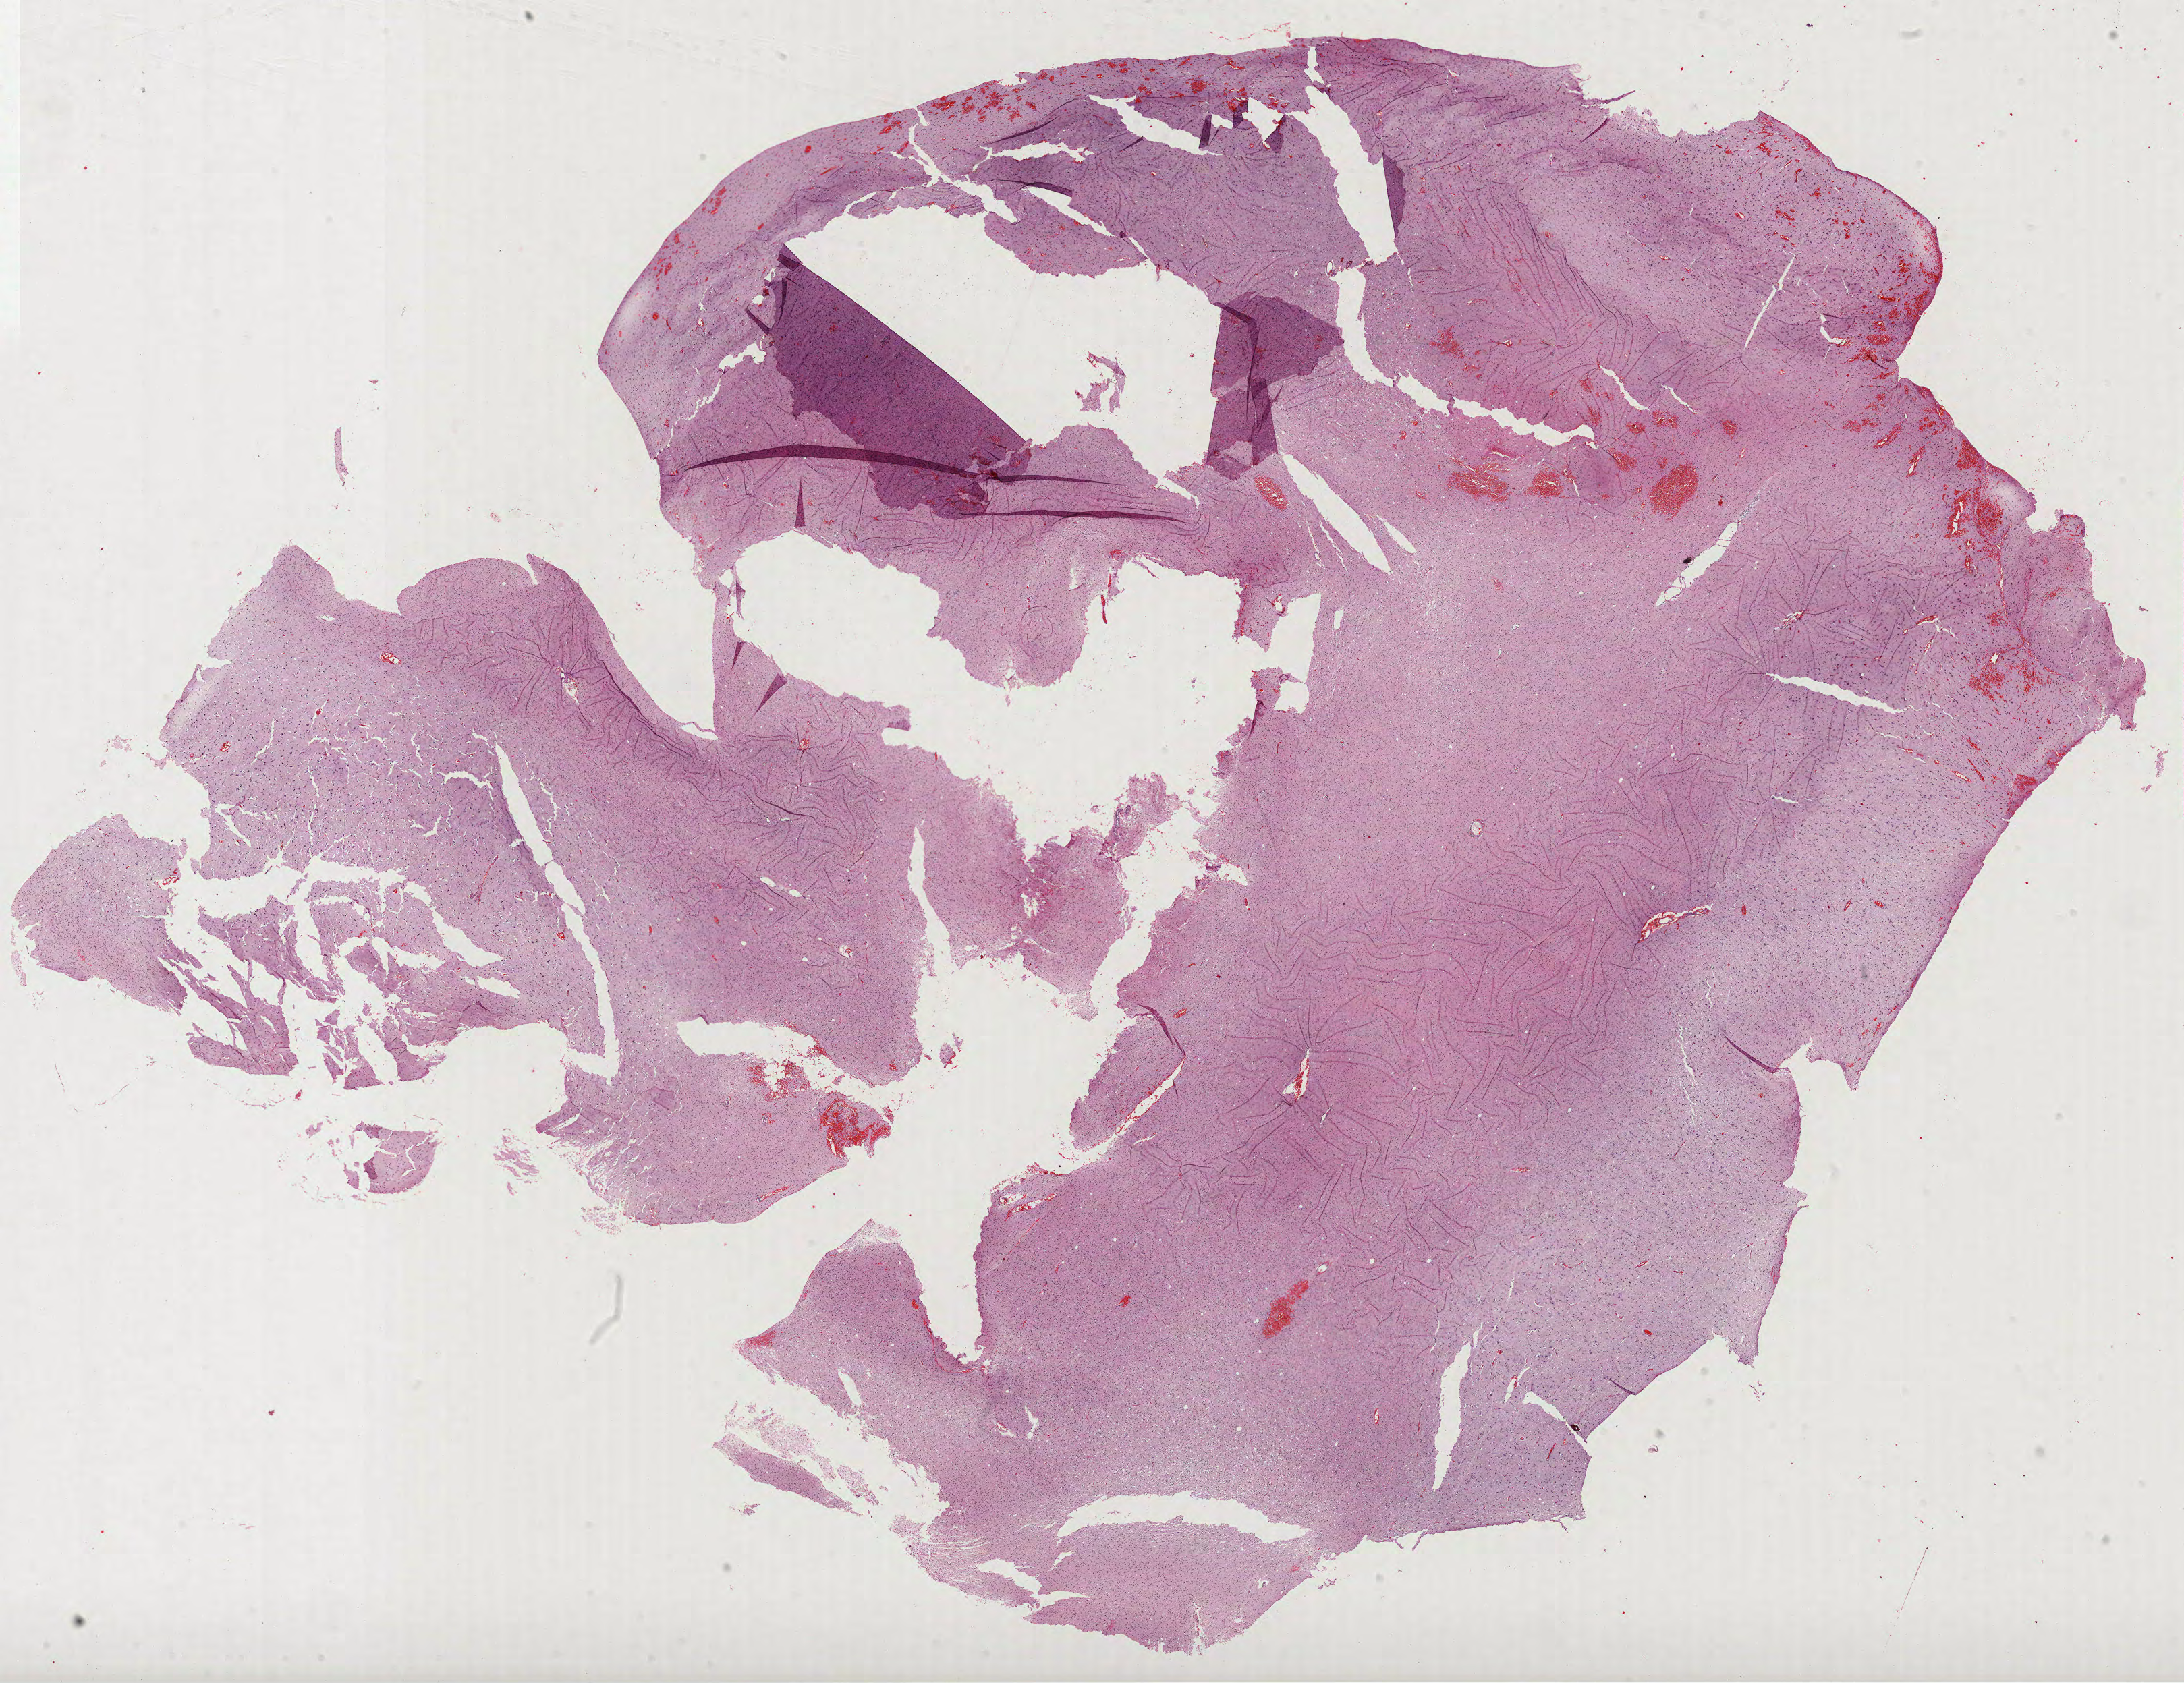
H&E-stained whole-slide image — shown as a low-resolution overview of the whole scanned area (about 26.1 x 20.1 mm, acquisition: 40x scan); FFPE section; primary tumour sample from the brain. Patient: male, age at initial diagnosis 37 years.
Histologic diagnosis: Oligodendroglioma, NOS.